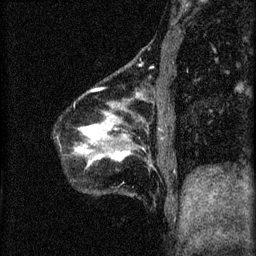
Breast MRI (dynamic contrast-enhanced), one sagittal slice. Position 12 of 60 along the scan axis. 3 images stored at this slice position (order not interpretable as contrast timing). 1.5 T. TE 4.2 ms, TR 8.2 ms. 2 mm slice thickness. 256 × 256 image matrix, field of view 180 × 180 mm. Patient: female, 40 years.
Structures marked on this image (semi-automatic segmentation, software-assisted and operator-edited):
- analysis volume of interest (the breast-tissue region the enhancement analysis was run in; not a lesion): bounding box <76,90,171,169> (left, top, right, bottom; pixels)
- tumour enhancement mask (voxels above the 70 % enhancement threshold inside the analysis volume of interest): <76,90,129,161>